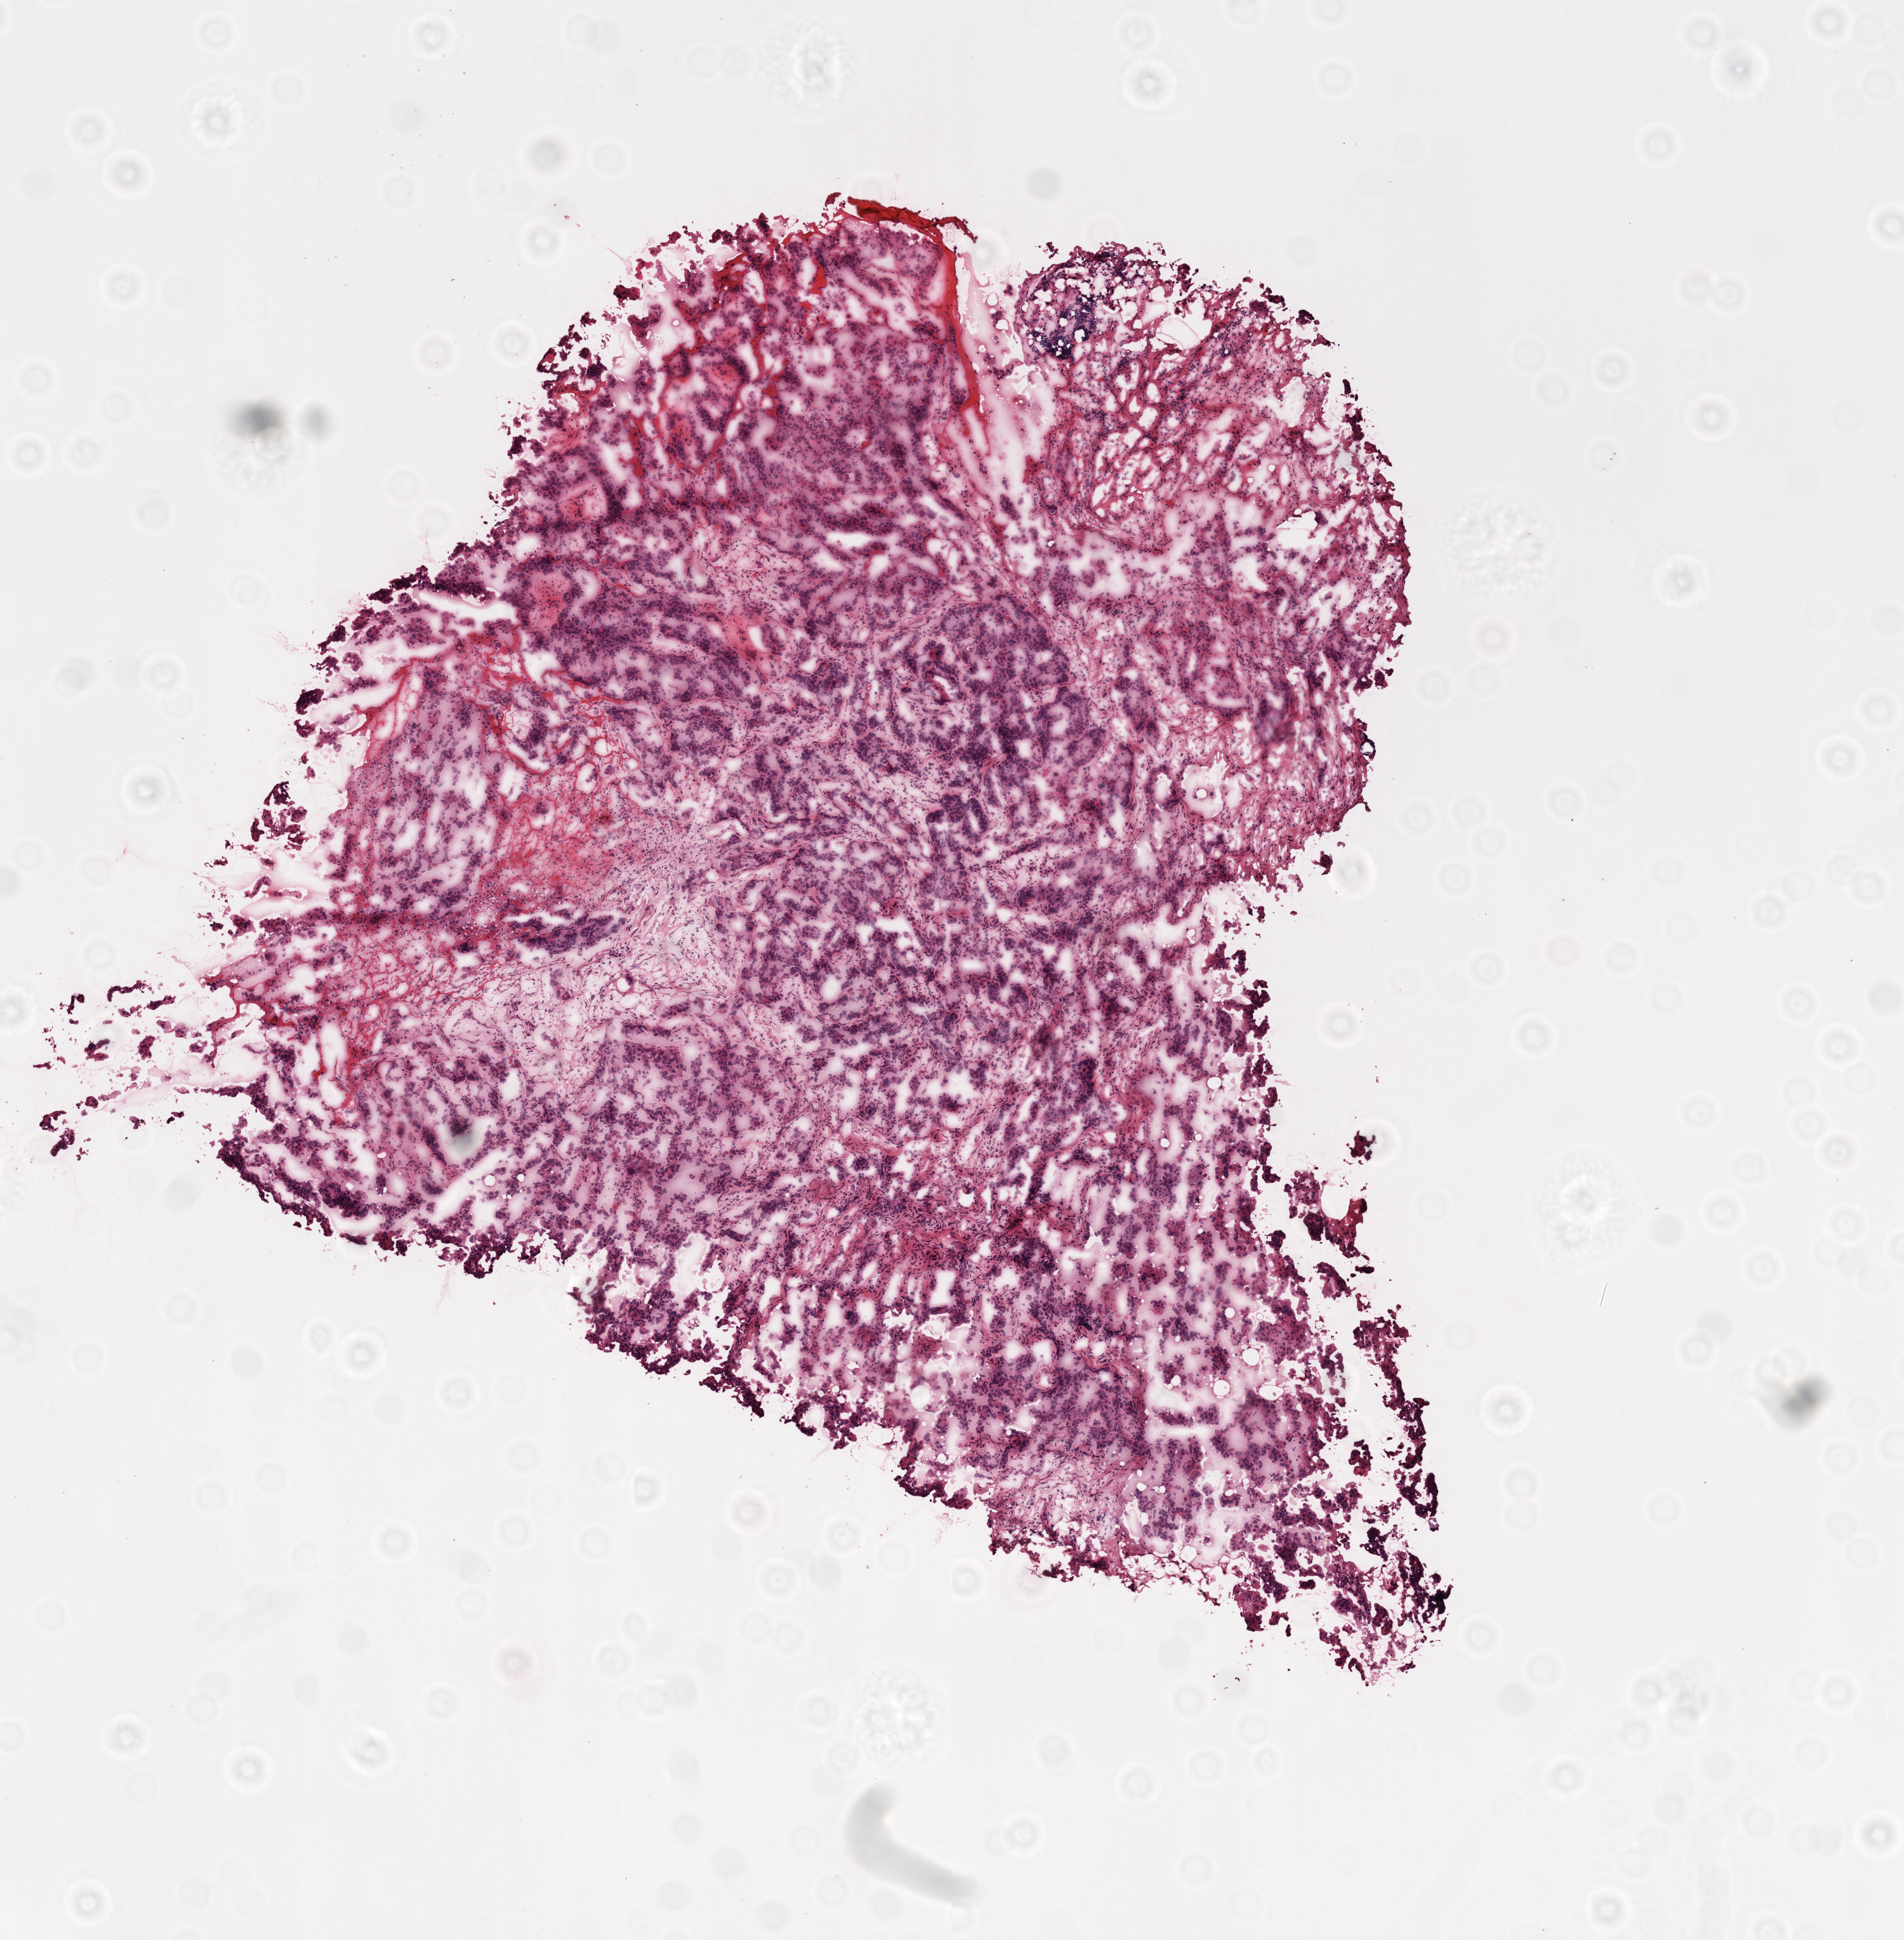
Whole-slide histology image, H&E-stained — low-resolution overview of the scanned area, about 6.0 x 6.1 mm (slide scanned at 20x), frozen section, primary tumour sample from the ovary. Female patient; age at initial diagnosis 58 years. Histologic grade: G2 (moderately differentiated). Slide review estimates, as recorded: tumour cells 60%, tumour nuclei 80%, normal cells 0%, stromal cells 40%, necrosis 0%.
FIGO stage: IIIC. Histologic diagnosis: Serous cystadenocarcinoma, NOS.